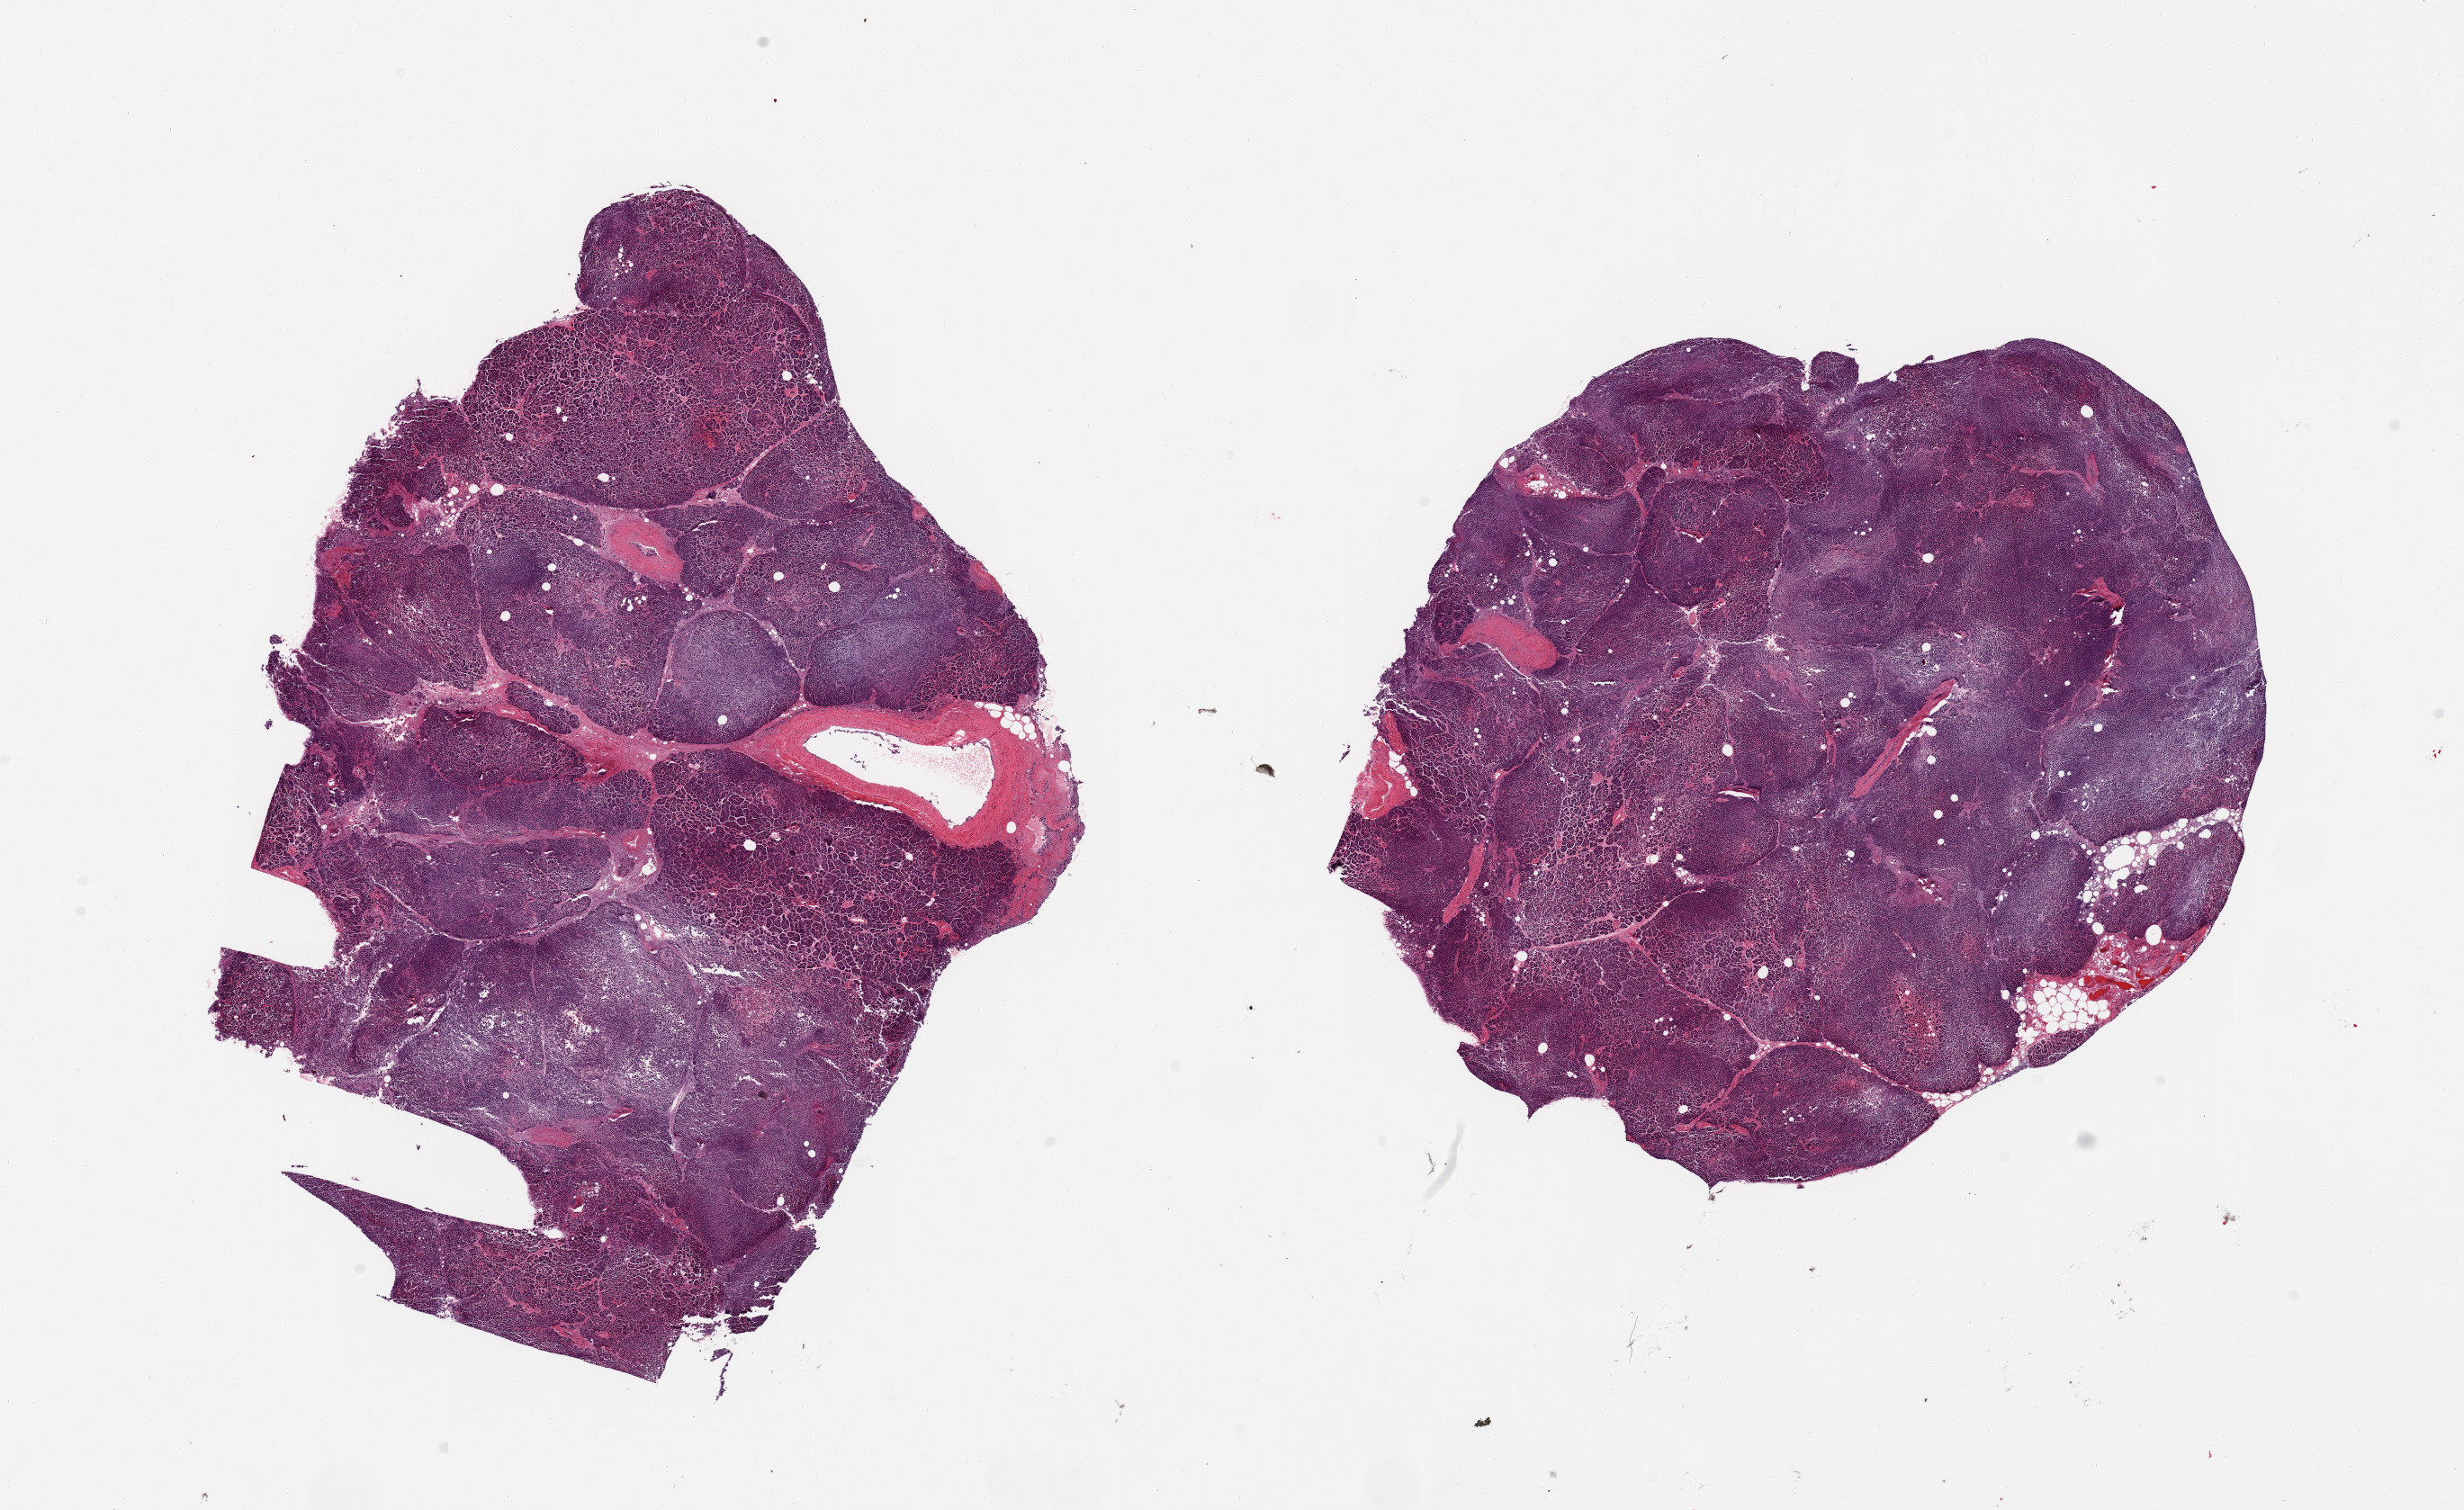
H&E whole-slide image, whole scanned area (about 21.7 x 13.3 mm) shown as a low-resolution overview. PAXgene-fixed paraffin-embedded (PFPE) section. Target tissue: pancreas. Donor tissue sample. Donor: male.
Pathologist's review note for this sample: 2 pieces; focal areas are autolysis 2.